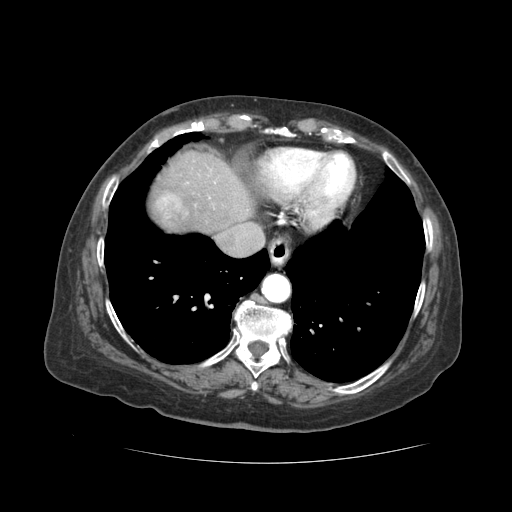
Contrast-enhanced abdominal CT (liver protocol), one axial slice; position 45 of 59 along the scan axis; soft-tissue window (W 400 / L 40 HU); 512 × 512 image matrix, field of view 380 × 380 mm. Case-level facts recorded for this patient, not image findings: diagnosis: hepatocellular carcinoma (patient treated with transarterial chemoembolisation; whether this scan precedes or follows treatment is not stated here); TNM stage (as recorded): Stage-I; Child-Pugh class: A; tumour nodularity: uninodular.
Structures marked on this image (semi-automatic segmentation, software-assisted and operator-edited):
- liver parenchyma outside the tumour (the mass and vessels are separate outlines, so this box may not span the whole liver): bounding box (x1, y1, x2, y2) in pixels: (152, 150, 252, 232)
- mass: (155, 194, 183, 222)